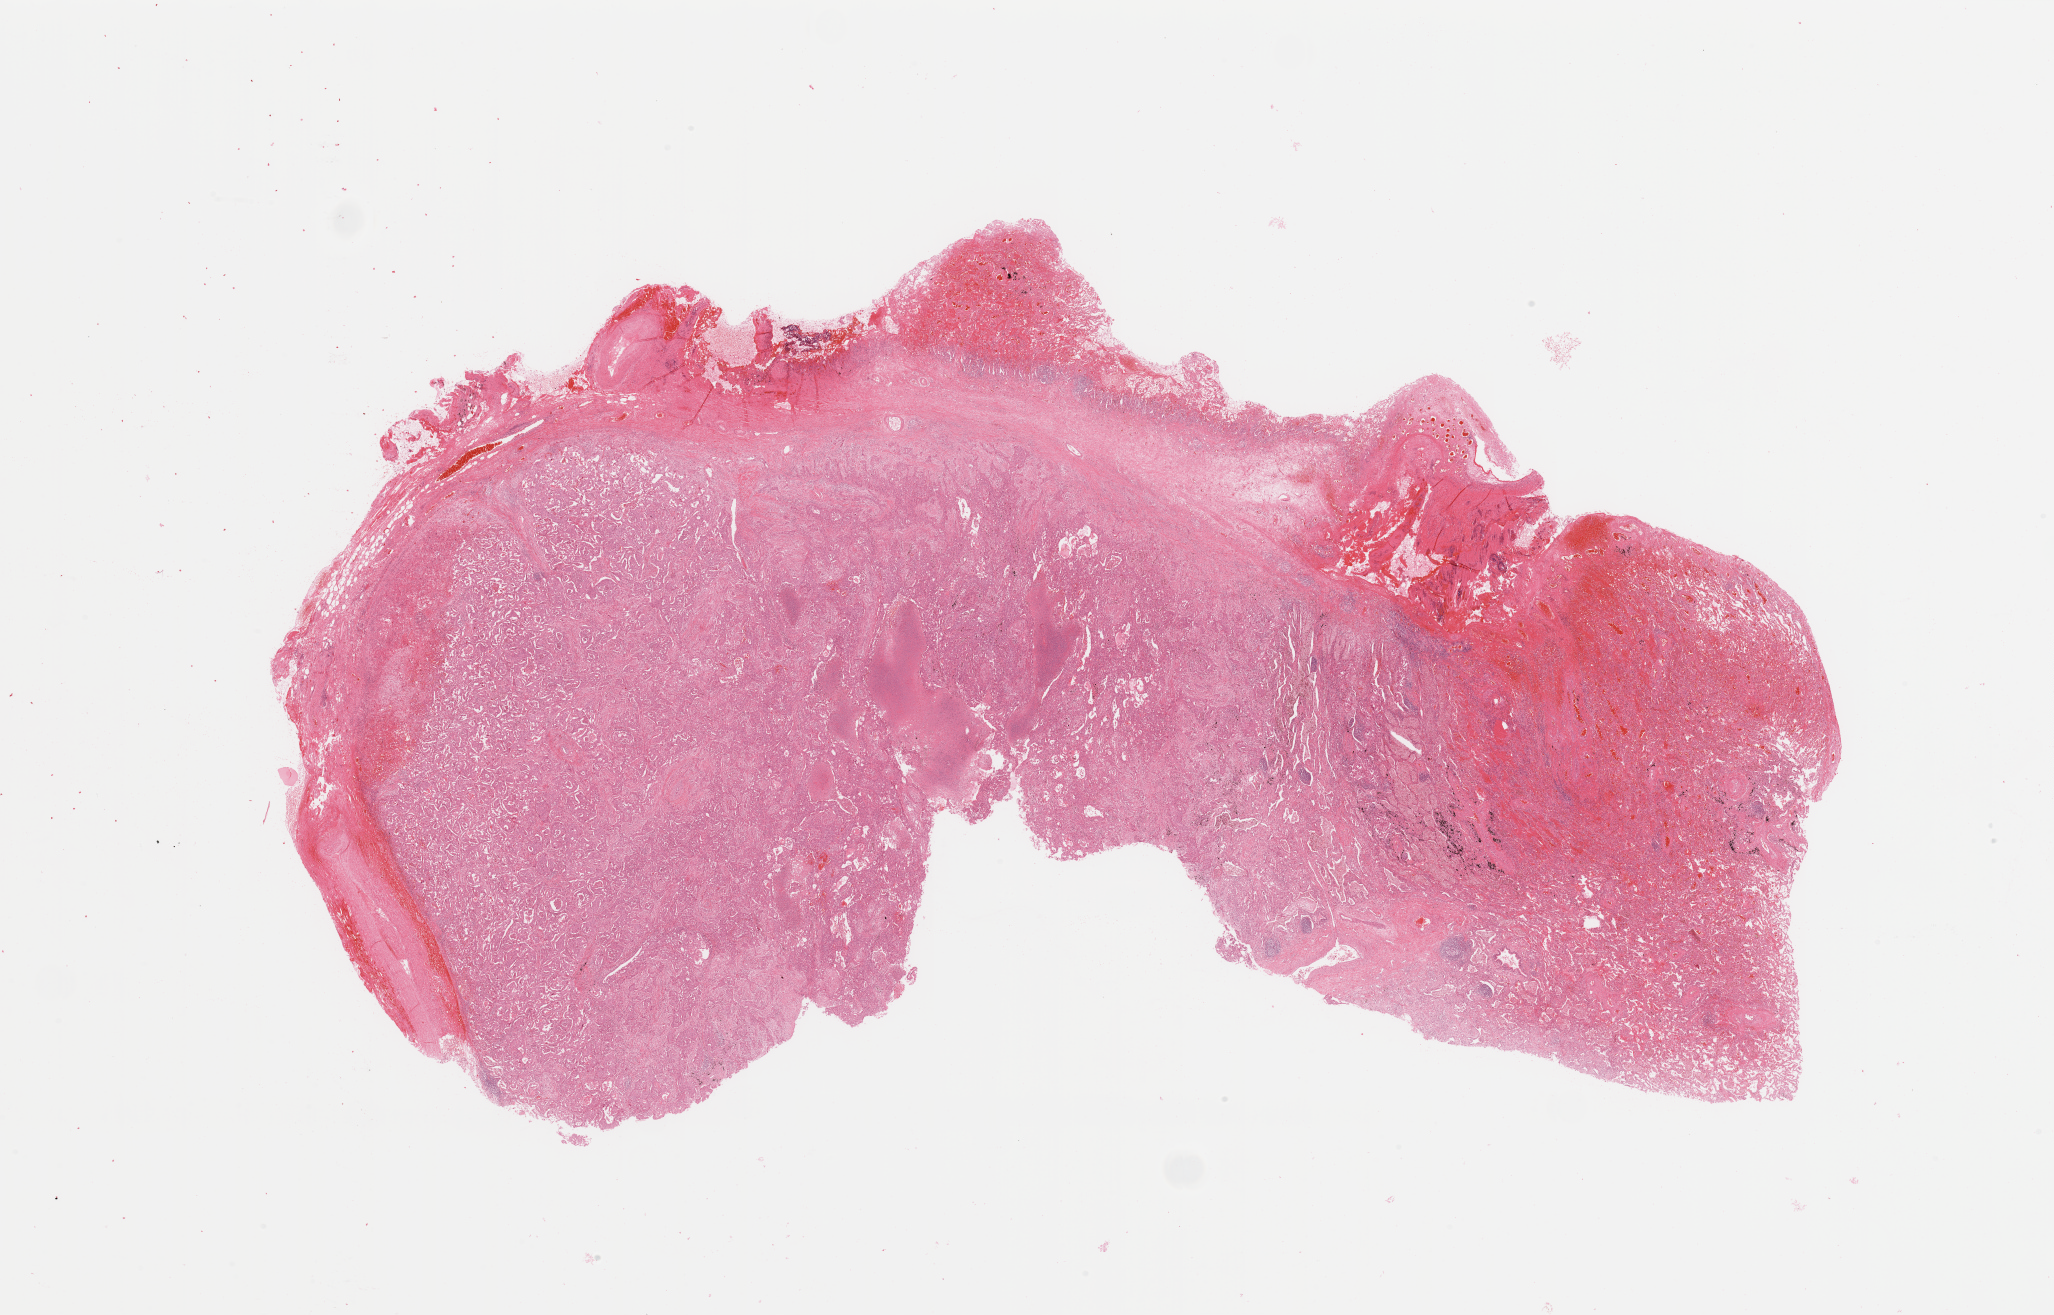
Whole-slide histology image, H&E-stained, shown as a low-resolution overview of the whole scanned area (about 32.5 x 20.8 mm, slide scanned at 20x); tumour tissue sample, sampled site: lung. 59-year-old male patient. Histologic grade: G3 (poorly differentiated). Pathologist review of this section (percent, as recorded): tumour nuclei 60%, necrosis 15%.
- AJCC pathologic stage: IIA
- histologic diagnosis: Adenocarcinoma, NOS